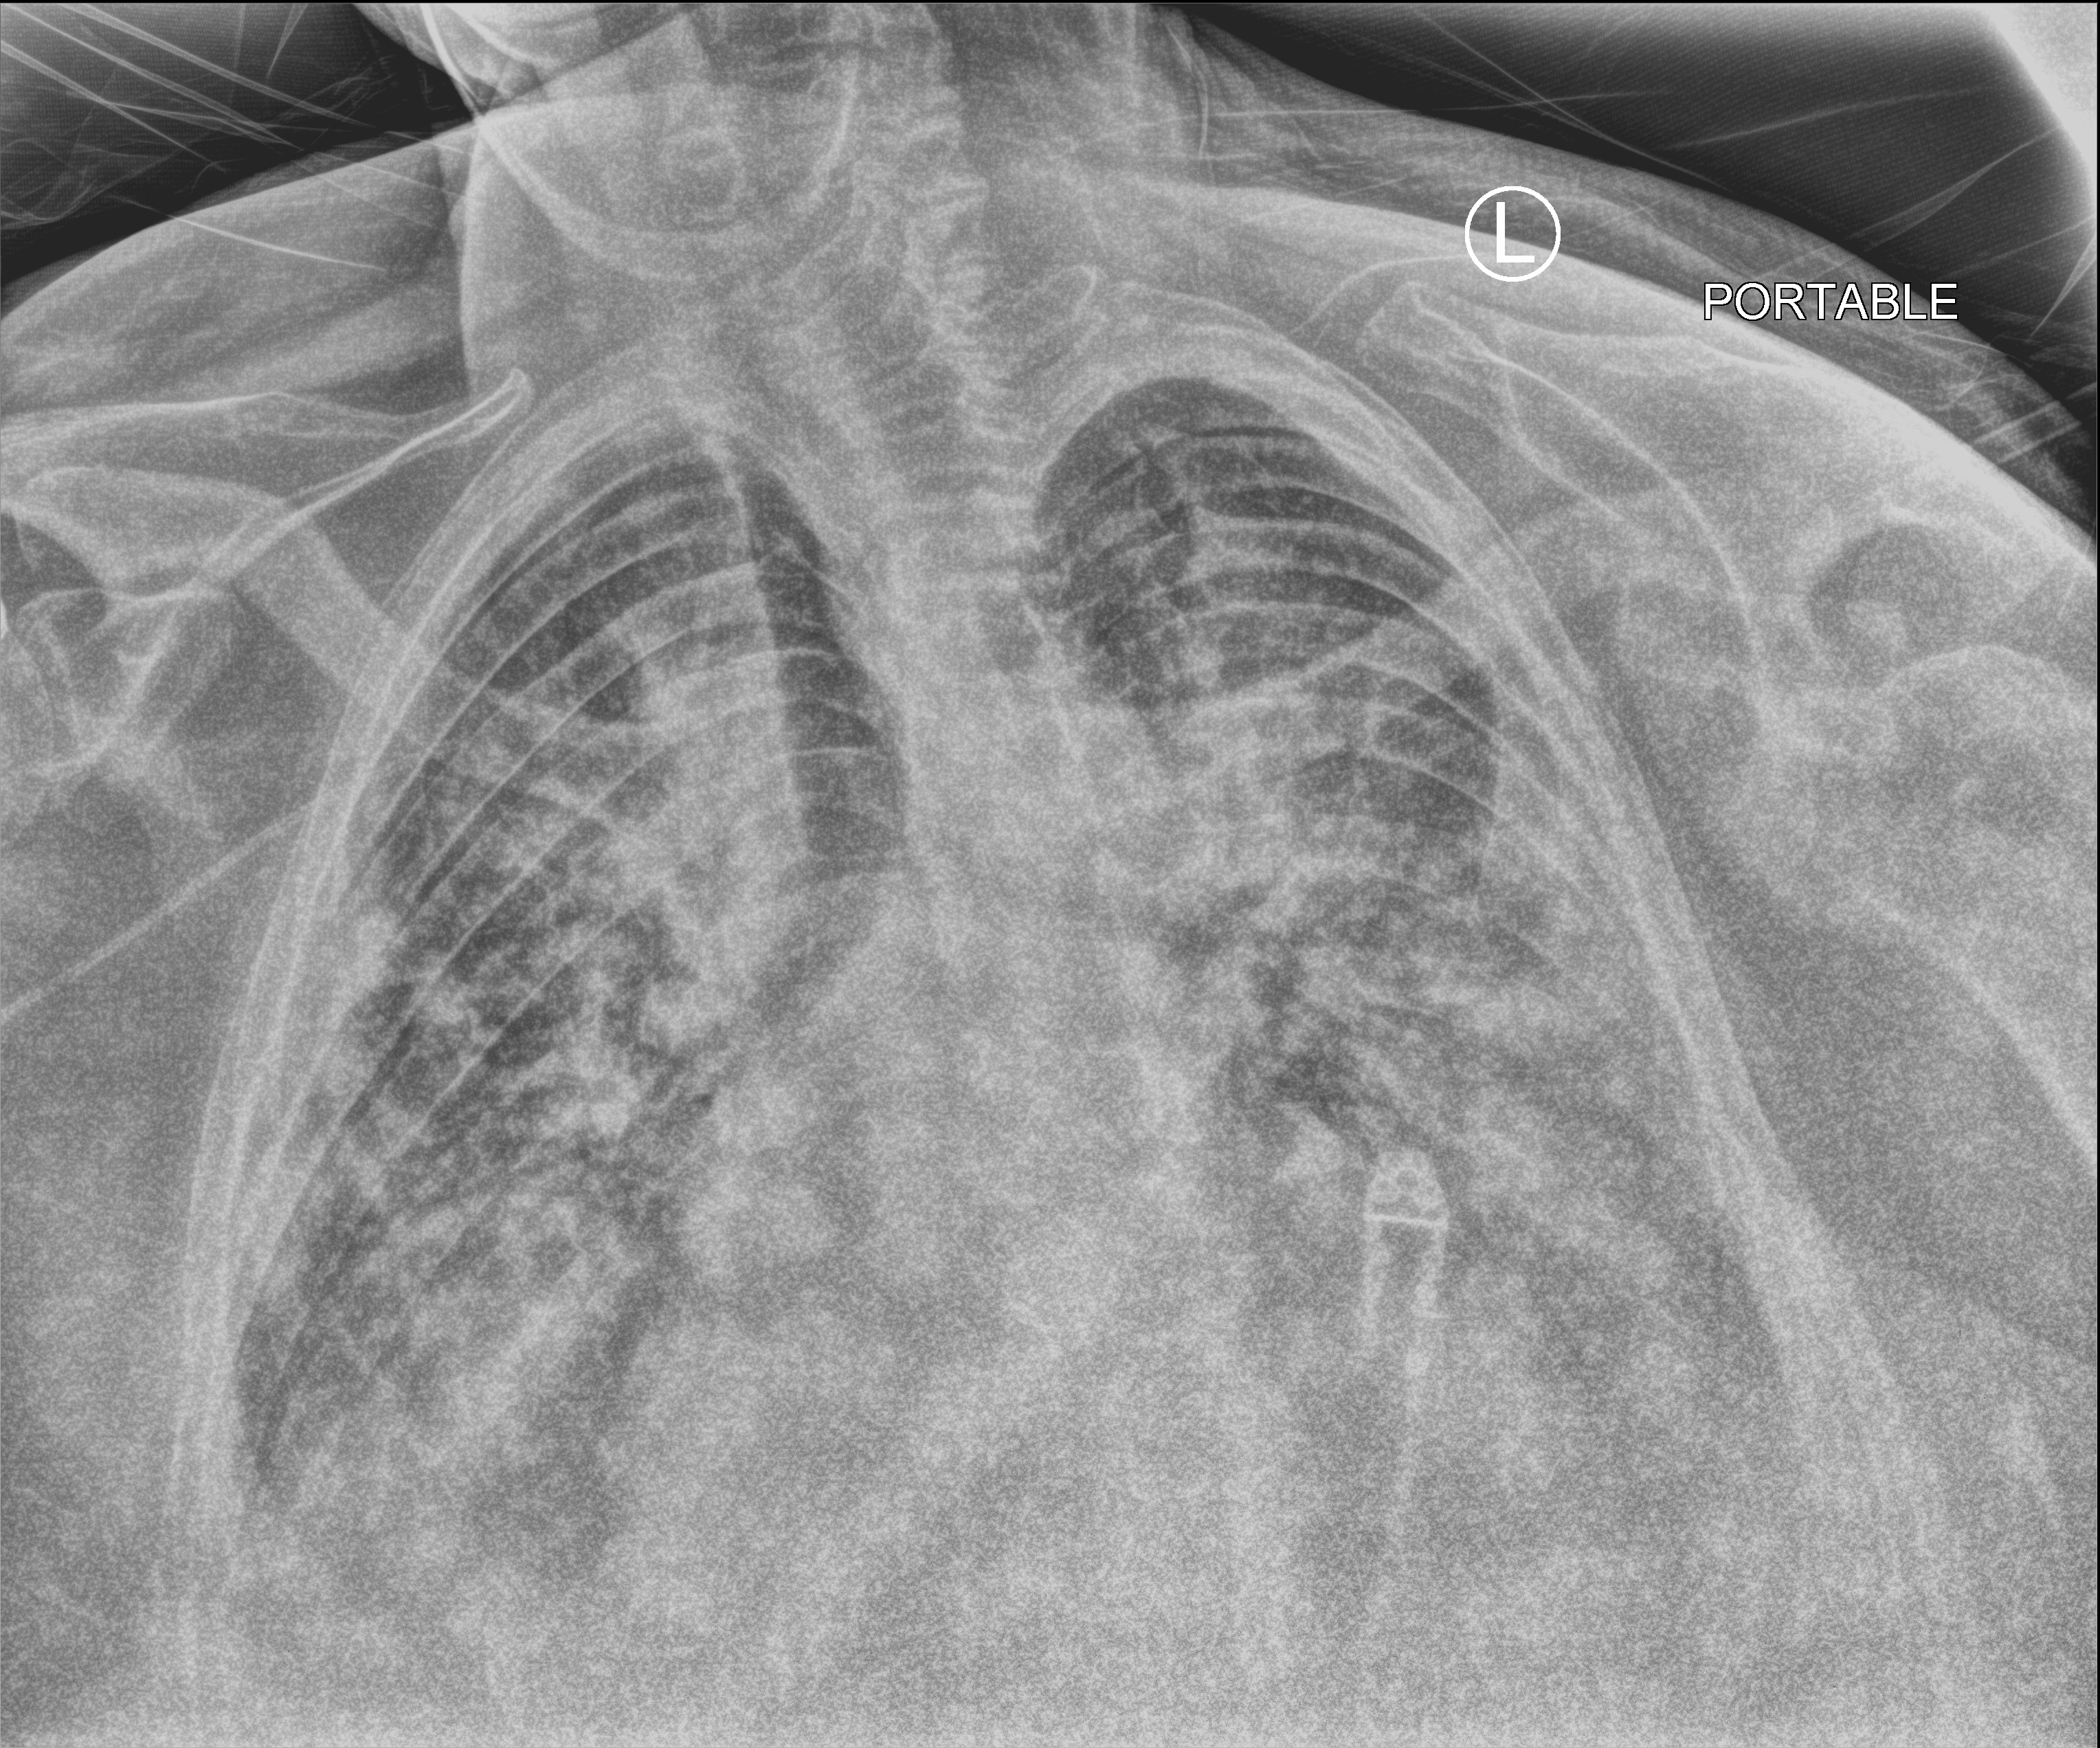
Chest X-ray (portable), anteroposterior (AP) projection. Patient hospitalised with COVID-19; male, aged 60–74 years.
Hospital-stay facts (about this admission, not read from this image; timing relative to this image not recorded): mechanically ventilated during this hospital stay: yes.